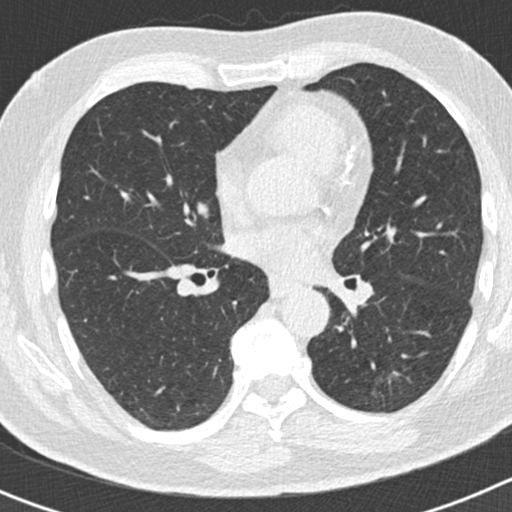
Axial slice from a low-dose chest CT screening exam. Second annual screen. Lung window (W 1500 / L -600 HU). 2 mm slice thickness. Standard (soft-tissue) reconstruction kernel (B30f). Slice 85 of 186 in the series. 512 × 512 image matrix, field of view 300 × 300 mm. Male participant, aged 66 years at enrolment. Former smoker at enrolment.
Expert reader's lesion annotation, bounding box [x1, y1, x2, y2] px = [352, 342, 411, 409]. The exam's reader record, not a measurement of the box and not confirmed to be the same lesion: non-calcified nodule or mass ≥4 mm, left lower lobe, 50 × 33 mm, smooth margins, pre-existing on the prior screen: yes; interval growth: yes. Later outcome: lung cancer diagnosed 440 days after this screen (after the third annual screen) — adenocarcinoma, NOS, left lower lobe, poorly differentiated (G3), stage IB (AJCC 6th edition), 38 mm at pathology.